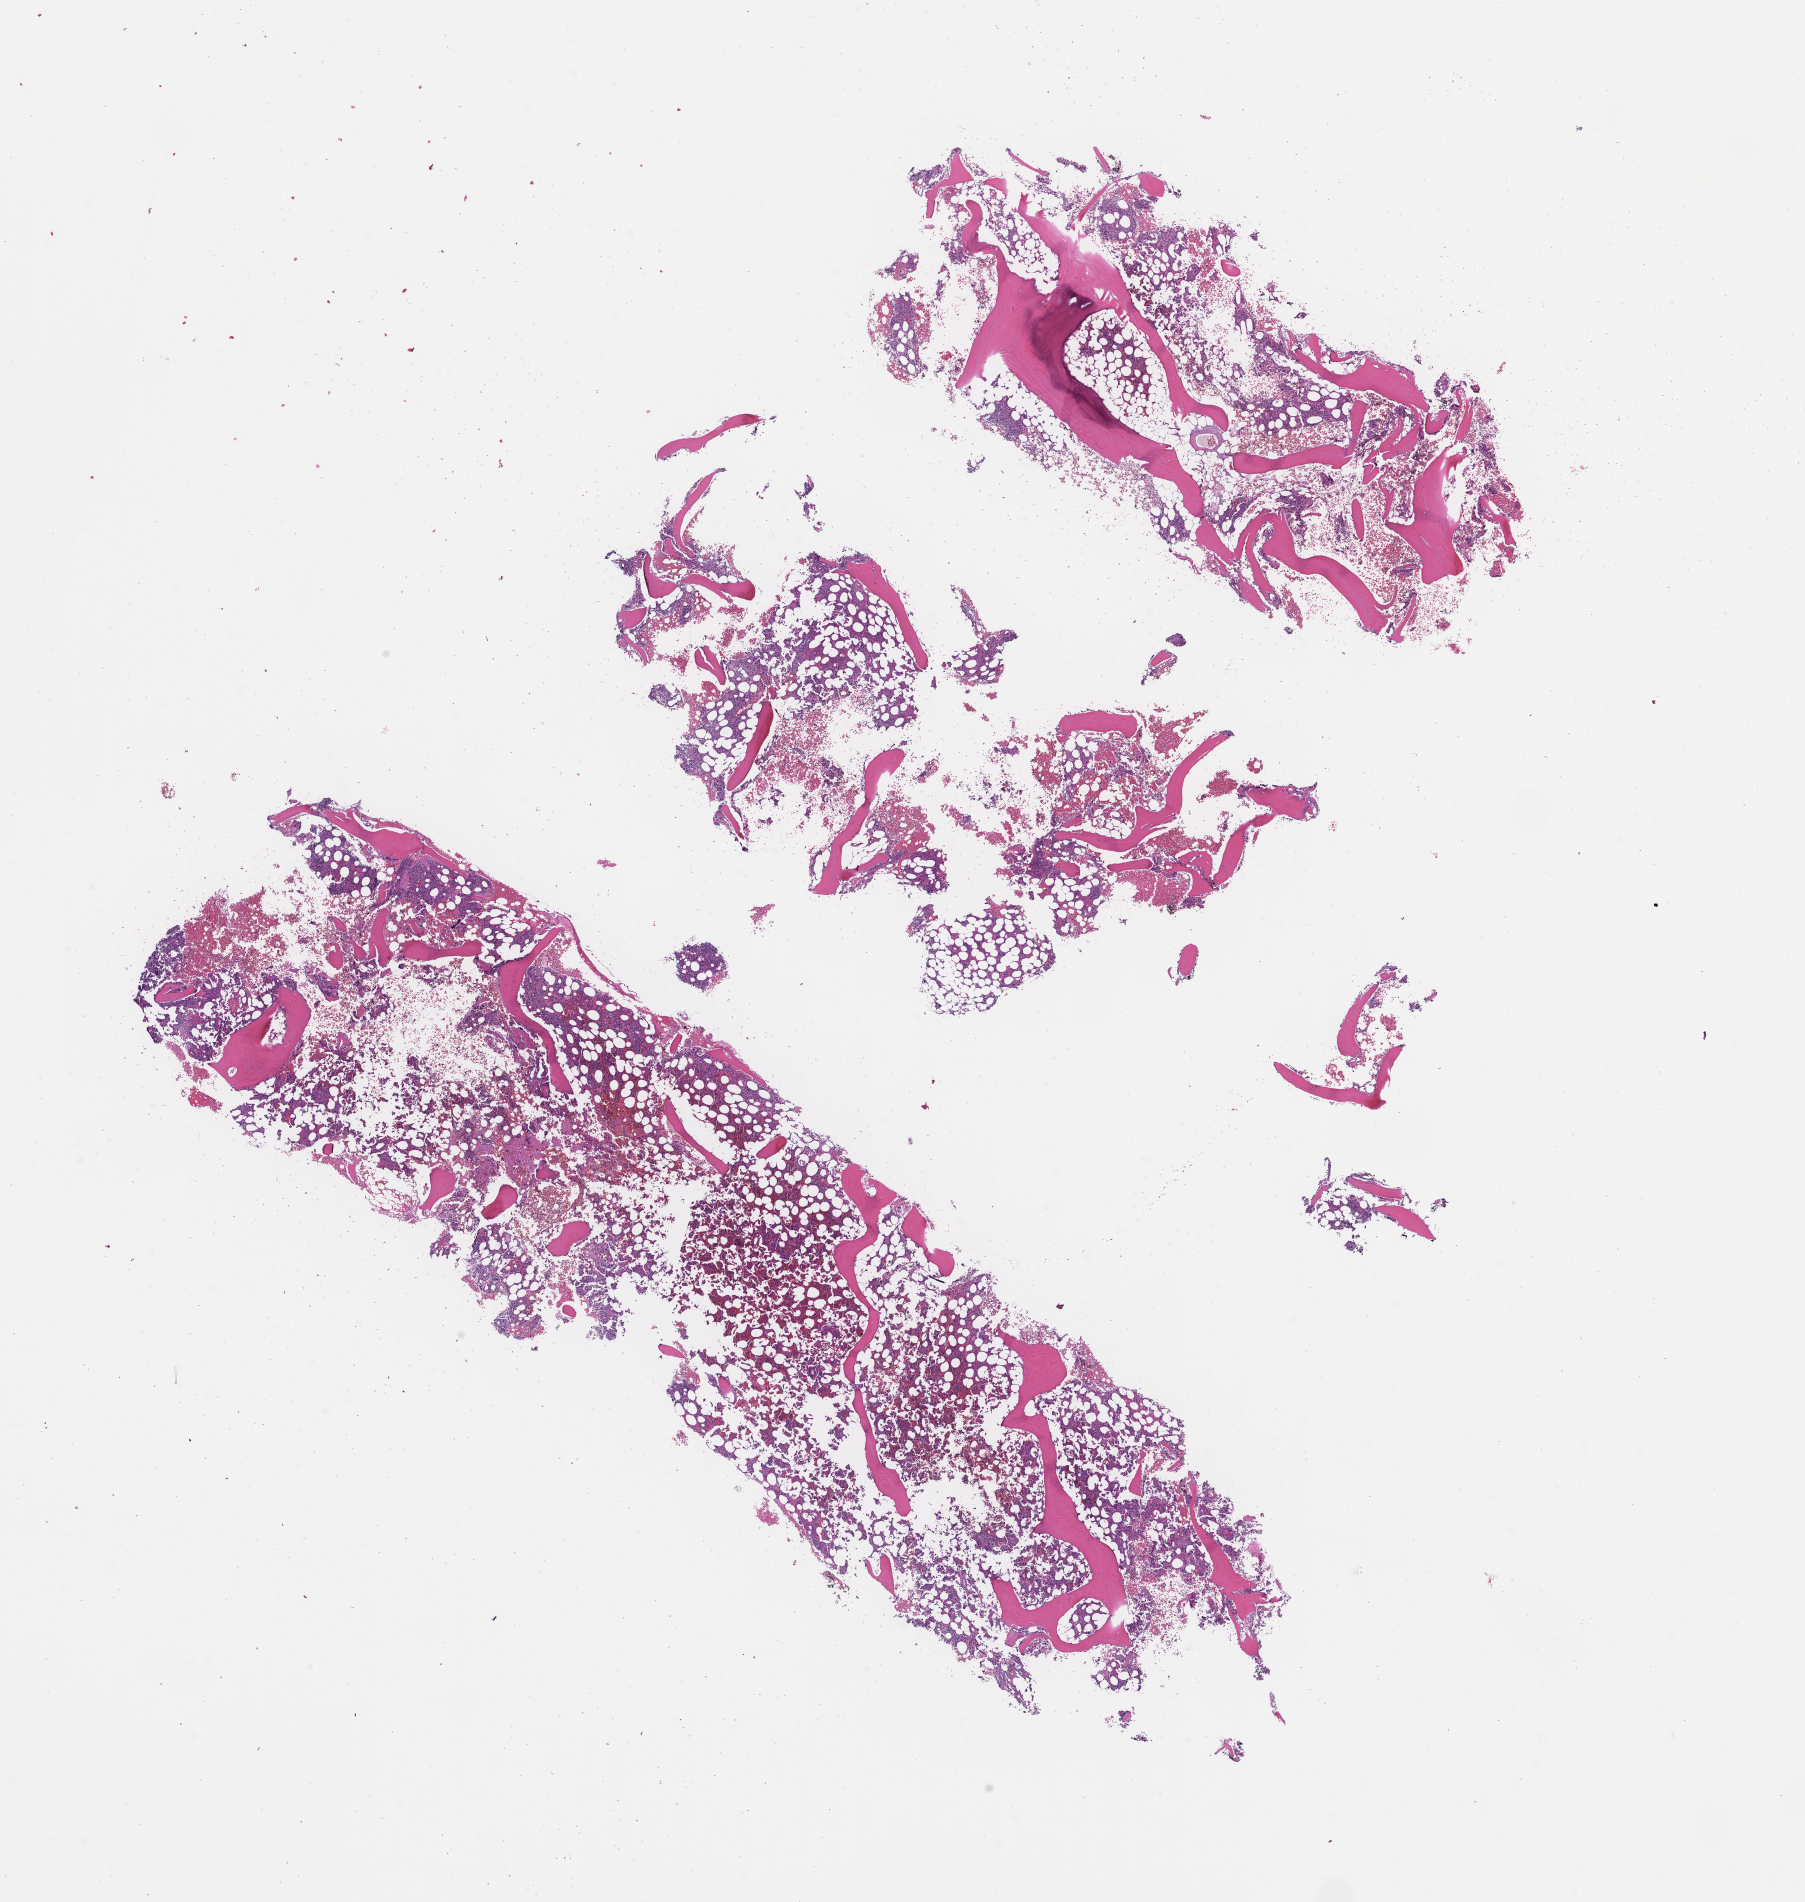
H&E whole-slide image — a low-resolution overview of the entire scanned area, about 14.6 x 15.4 mm. Formalin-fixed paraffin-embedded section. Site: bone marrow. Archival tissue. Male patient.
- this section: primary tumor
- diagnosis: Plasma Cell Myeloma